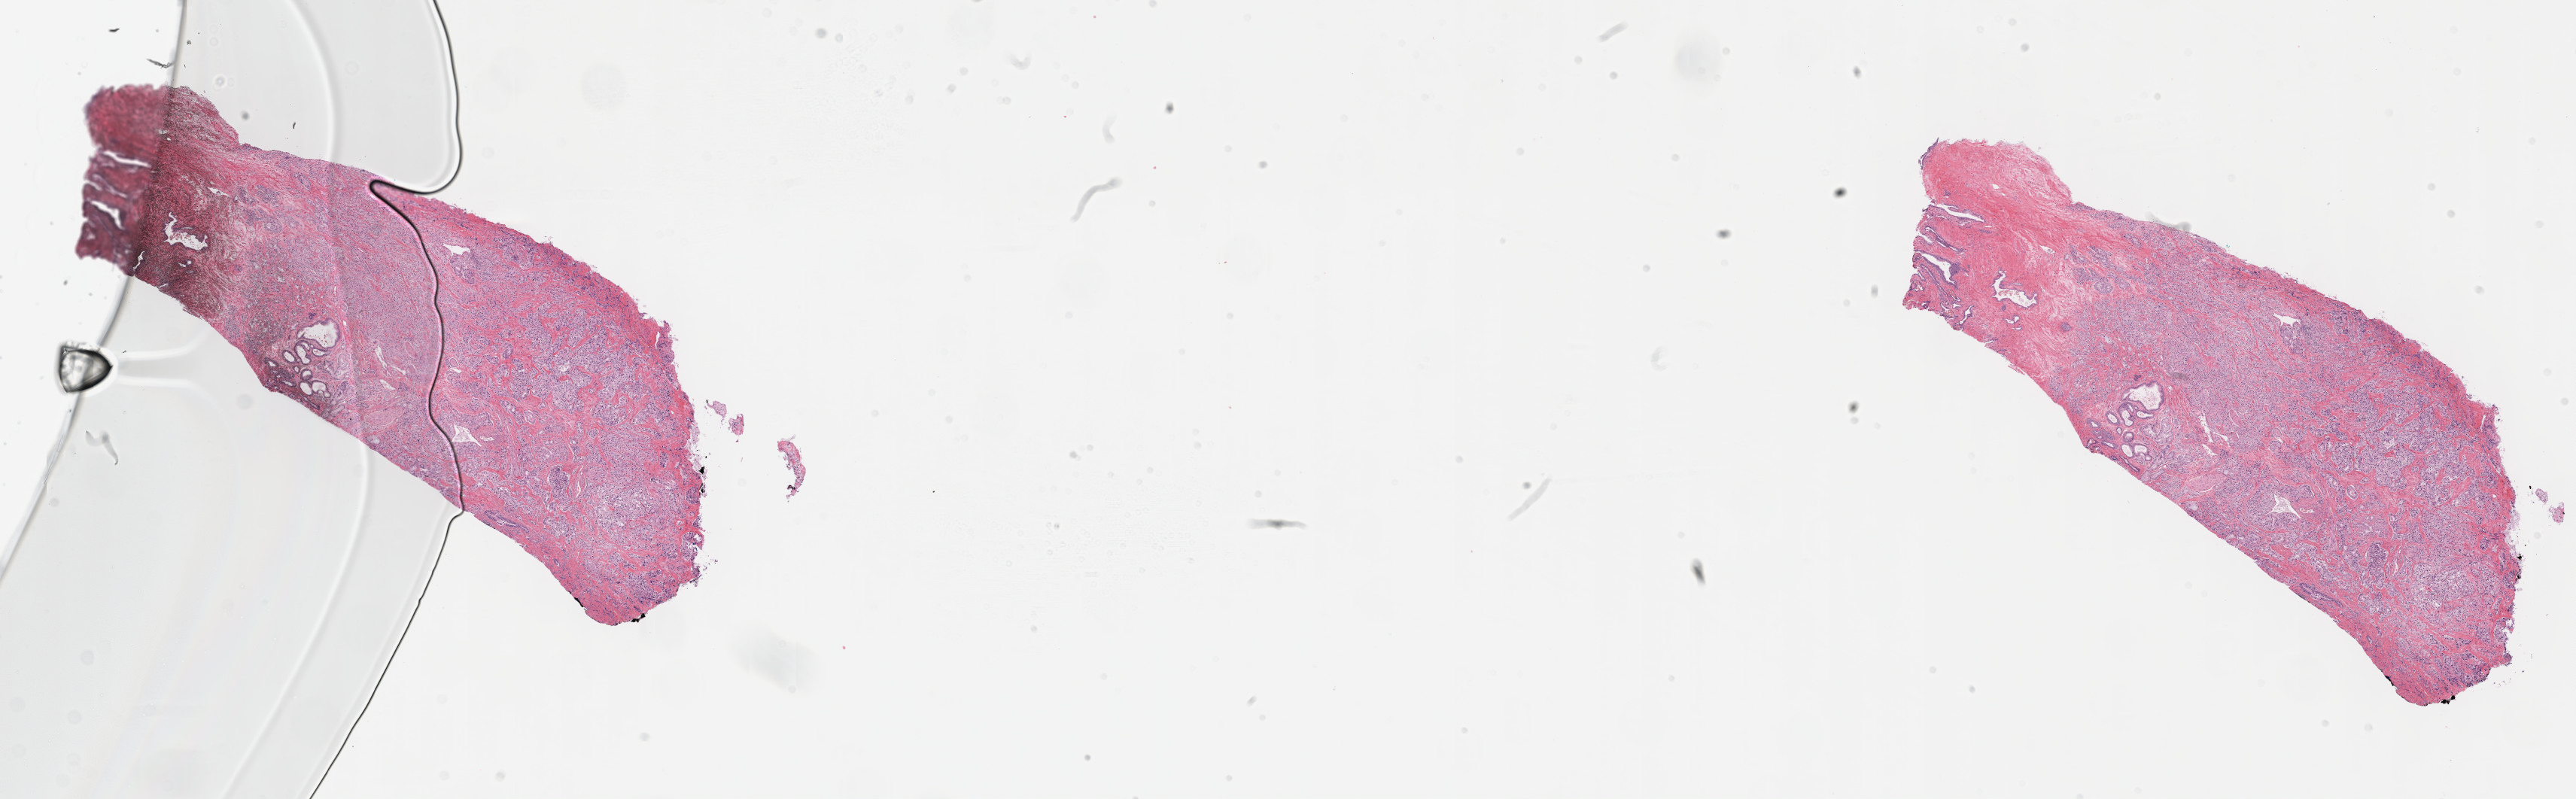
Digitized Hematoxylin and eosin (H&E) stained tissue section (whole slide), a low-resolution overview of the entire scanned area, about 27.7 x 8.6 mm; formalin-fixed paraffin-embedded (FFPE) diagnostic section; sample: primary tumour, prostate. Male, age 75 years at initial diagnosis. Gleason score: 7 (4+3). Slide review estimates, as recorded: tumour cells 60%, tumour nuclei 90%, normal cells 4%, stromal cells 35%, necrosis 1%. Infiltration values recorded for this section: lymphocyte infiltration 3%, monocyte infiltration 0%, neutrophil infiltration 0%.
* laterality: bilateral
* histologic diagnosis: Adenocarcinoma, NOS (prostate gland)
* lymph nodes positive (case pathology): 0 of 4 examined